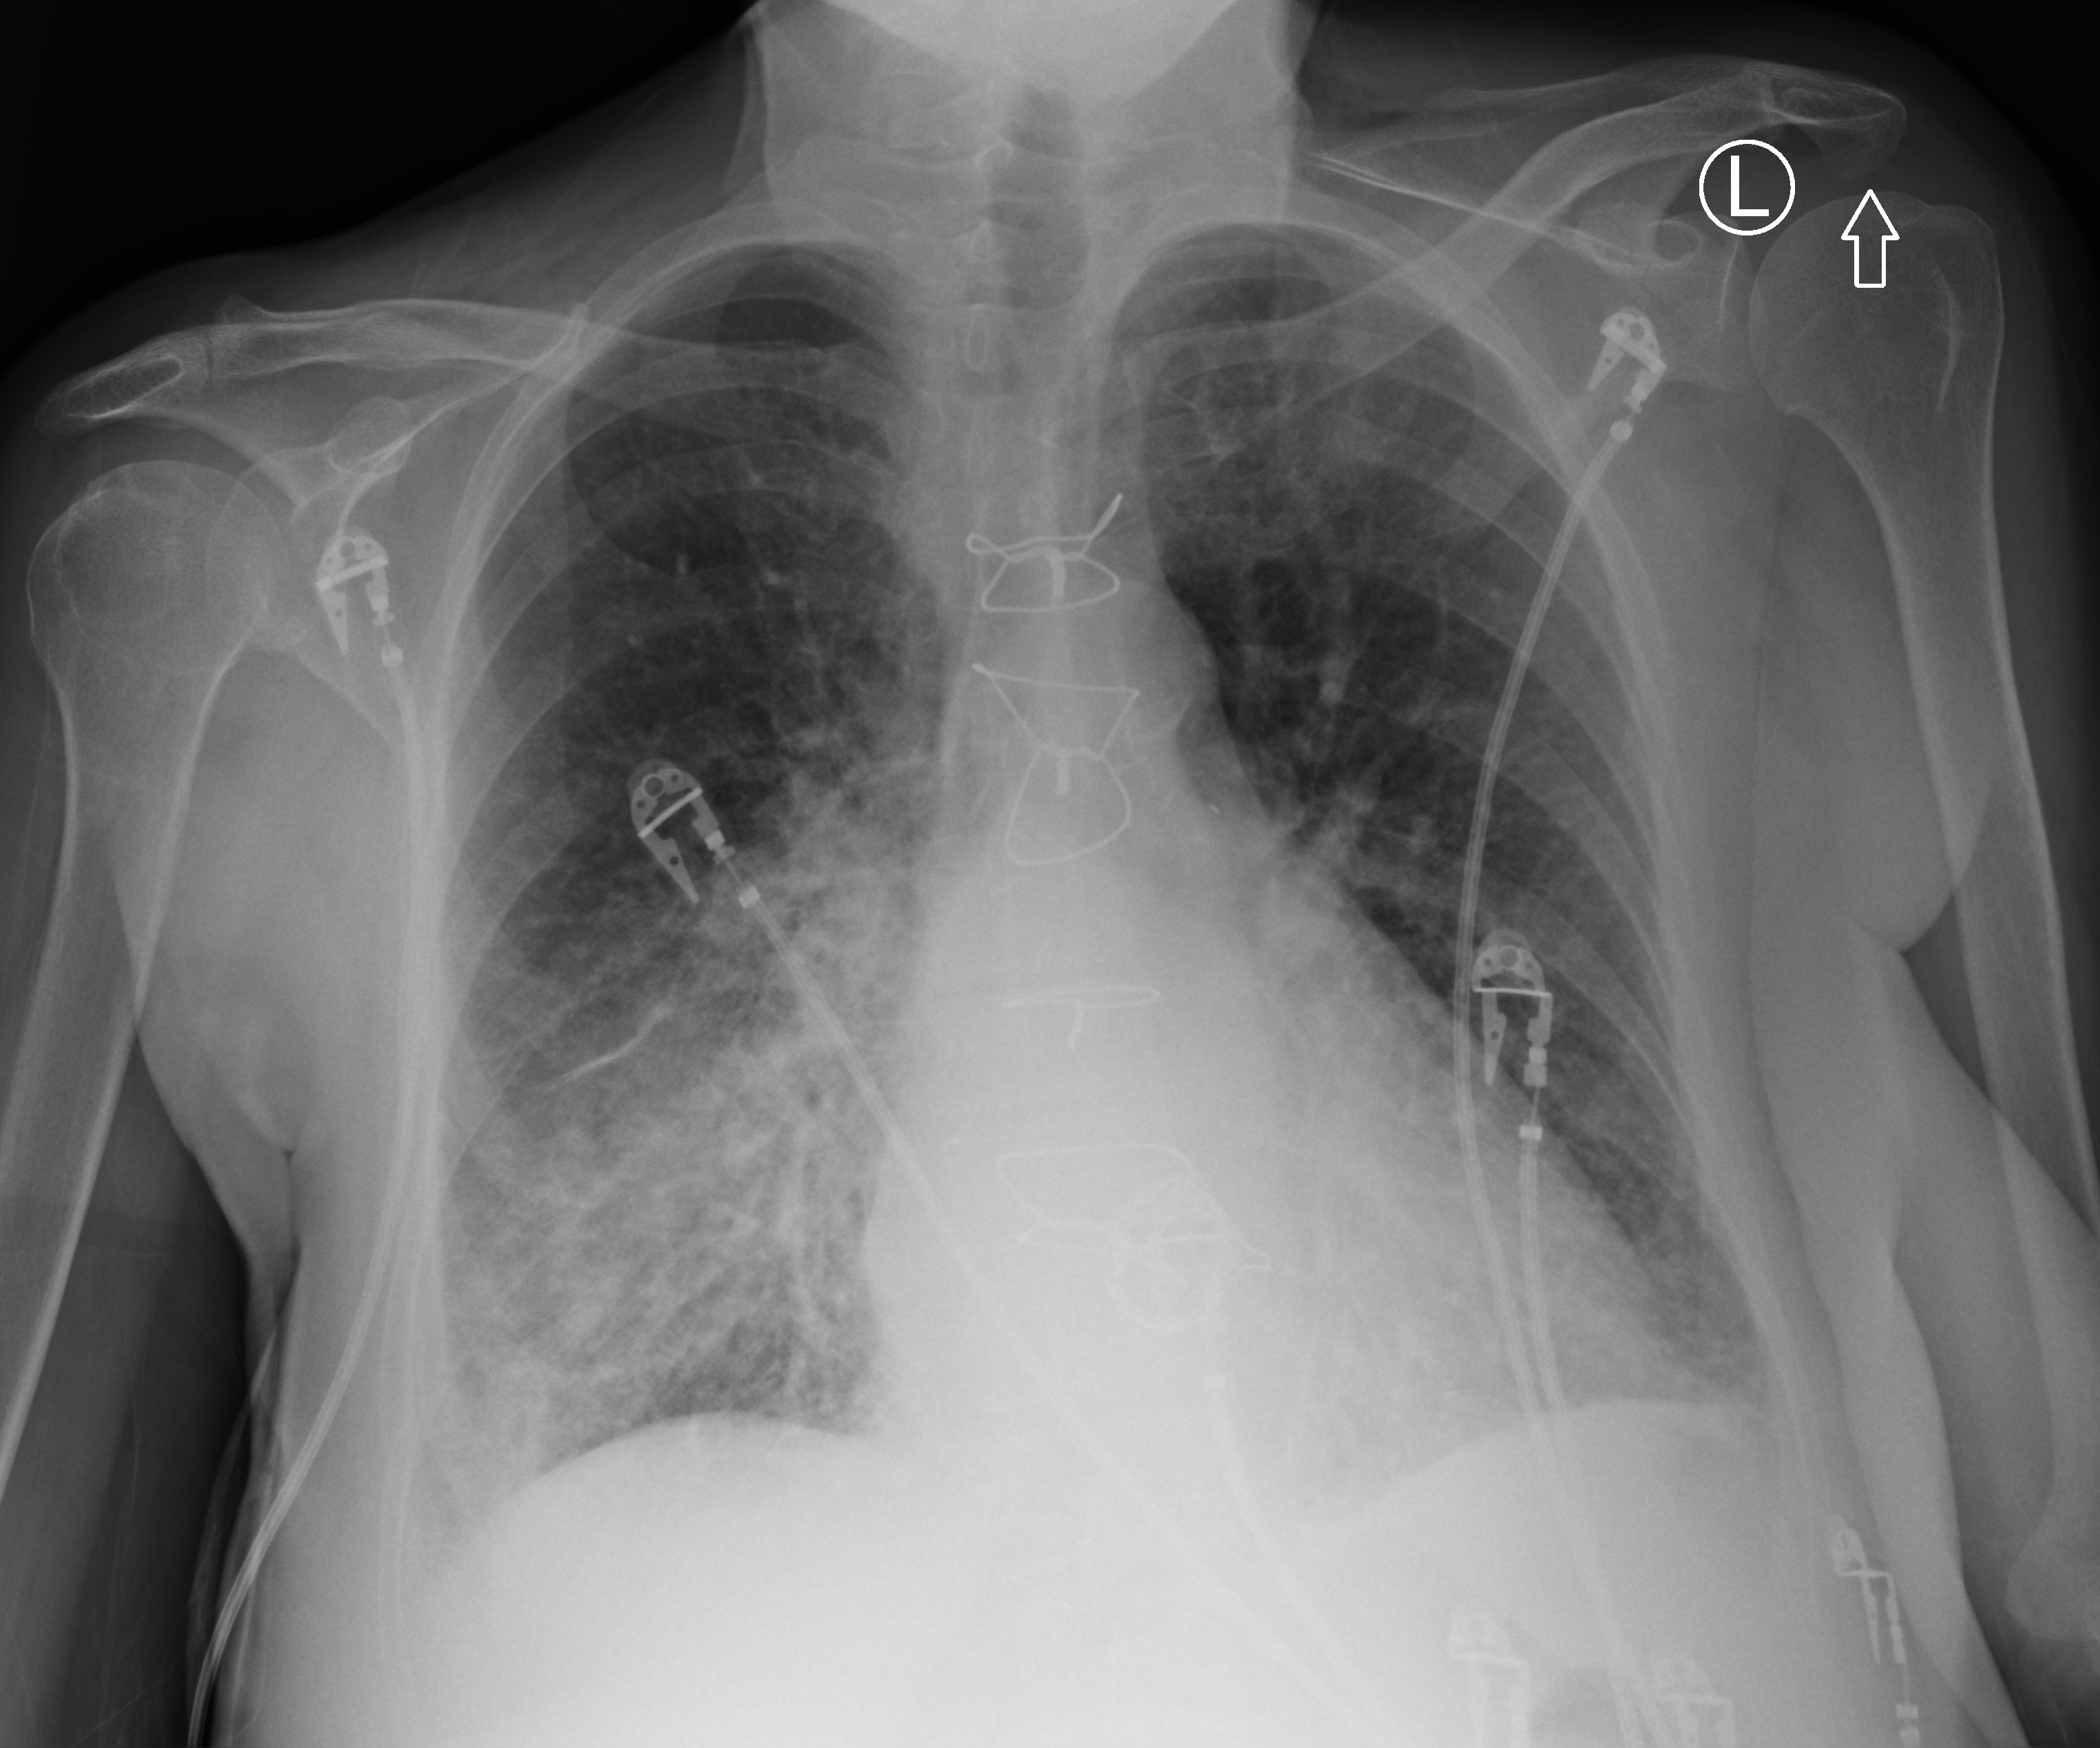
Chest X-ray (portable), anteroposterior (AP) projection. Female patient hospitalised with COVID-19, age 60–74 years.
Hospital-stay facts (about this admission, not read from this image; timing relative to this image not recorded):
- admitted to intensive care during this hospital stay: yes
- mechanically ventilated during this hospital stay: no